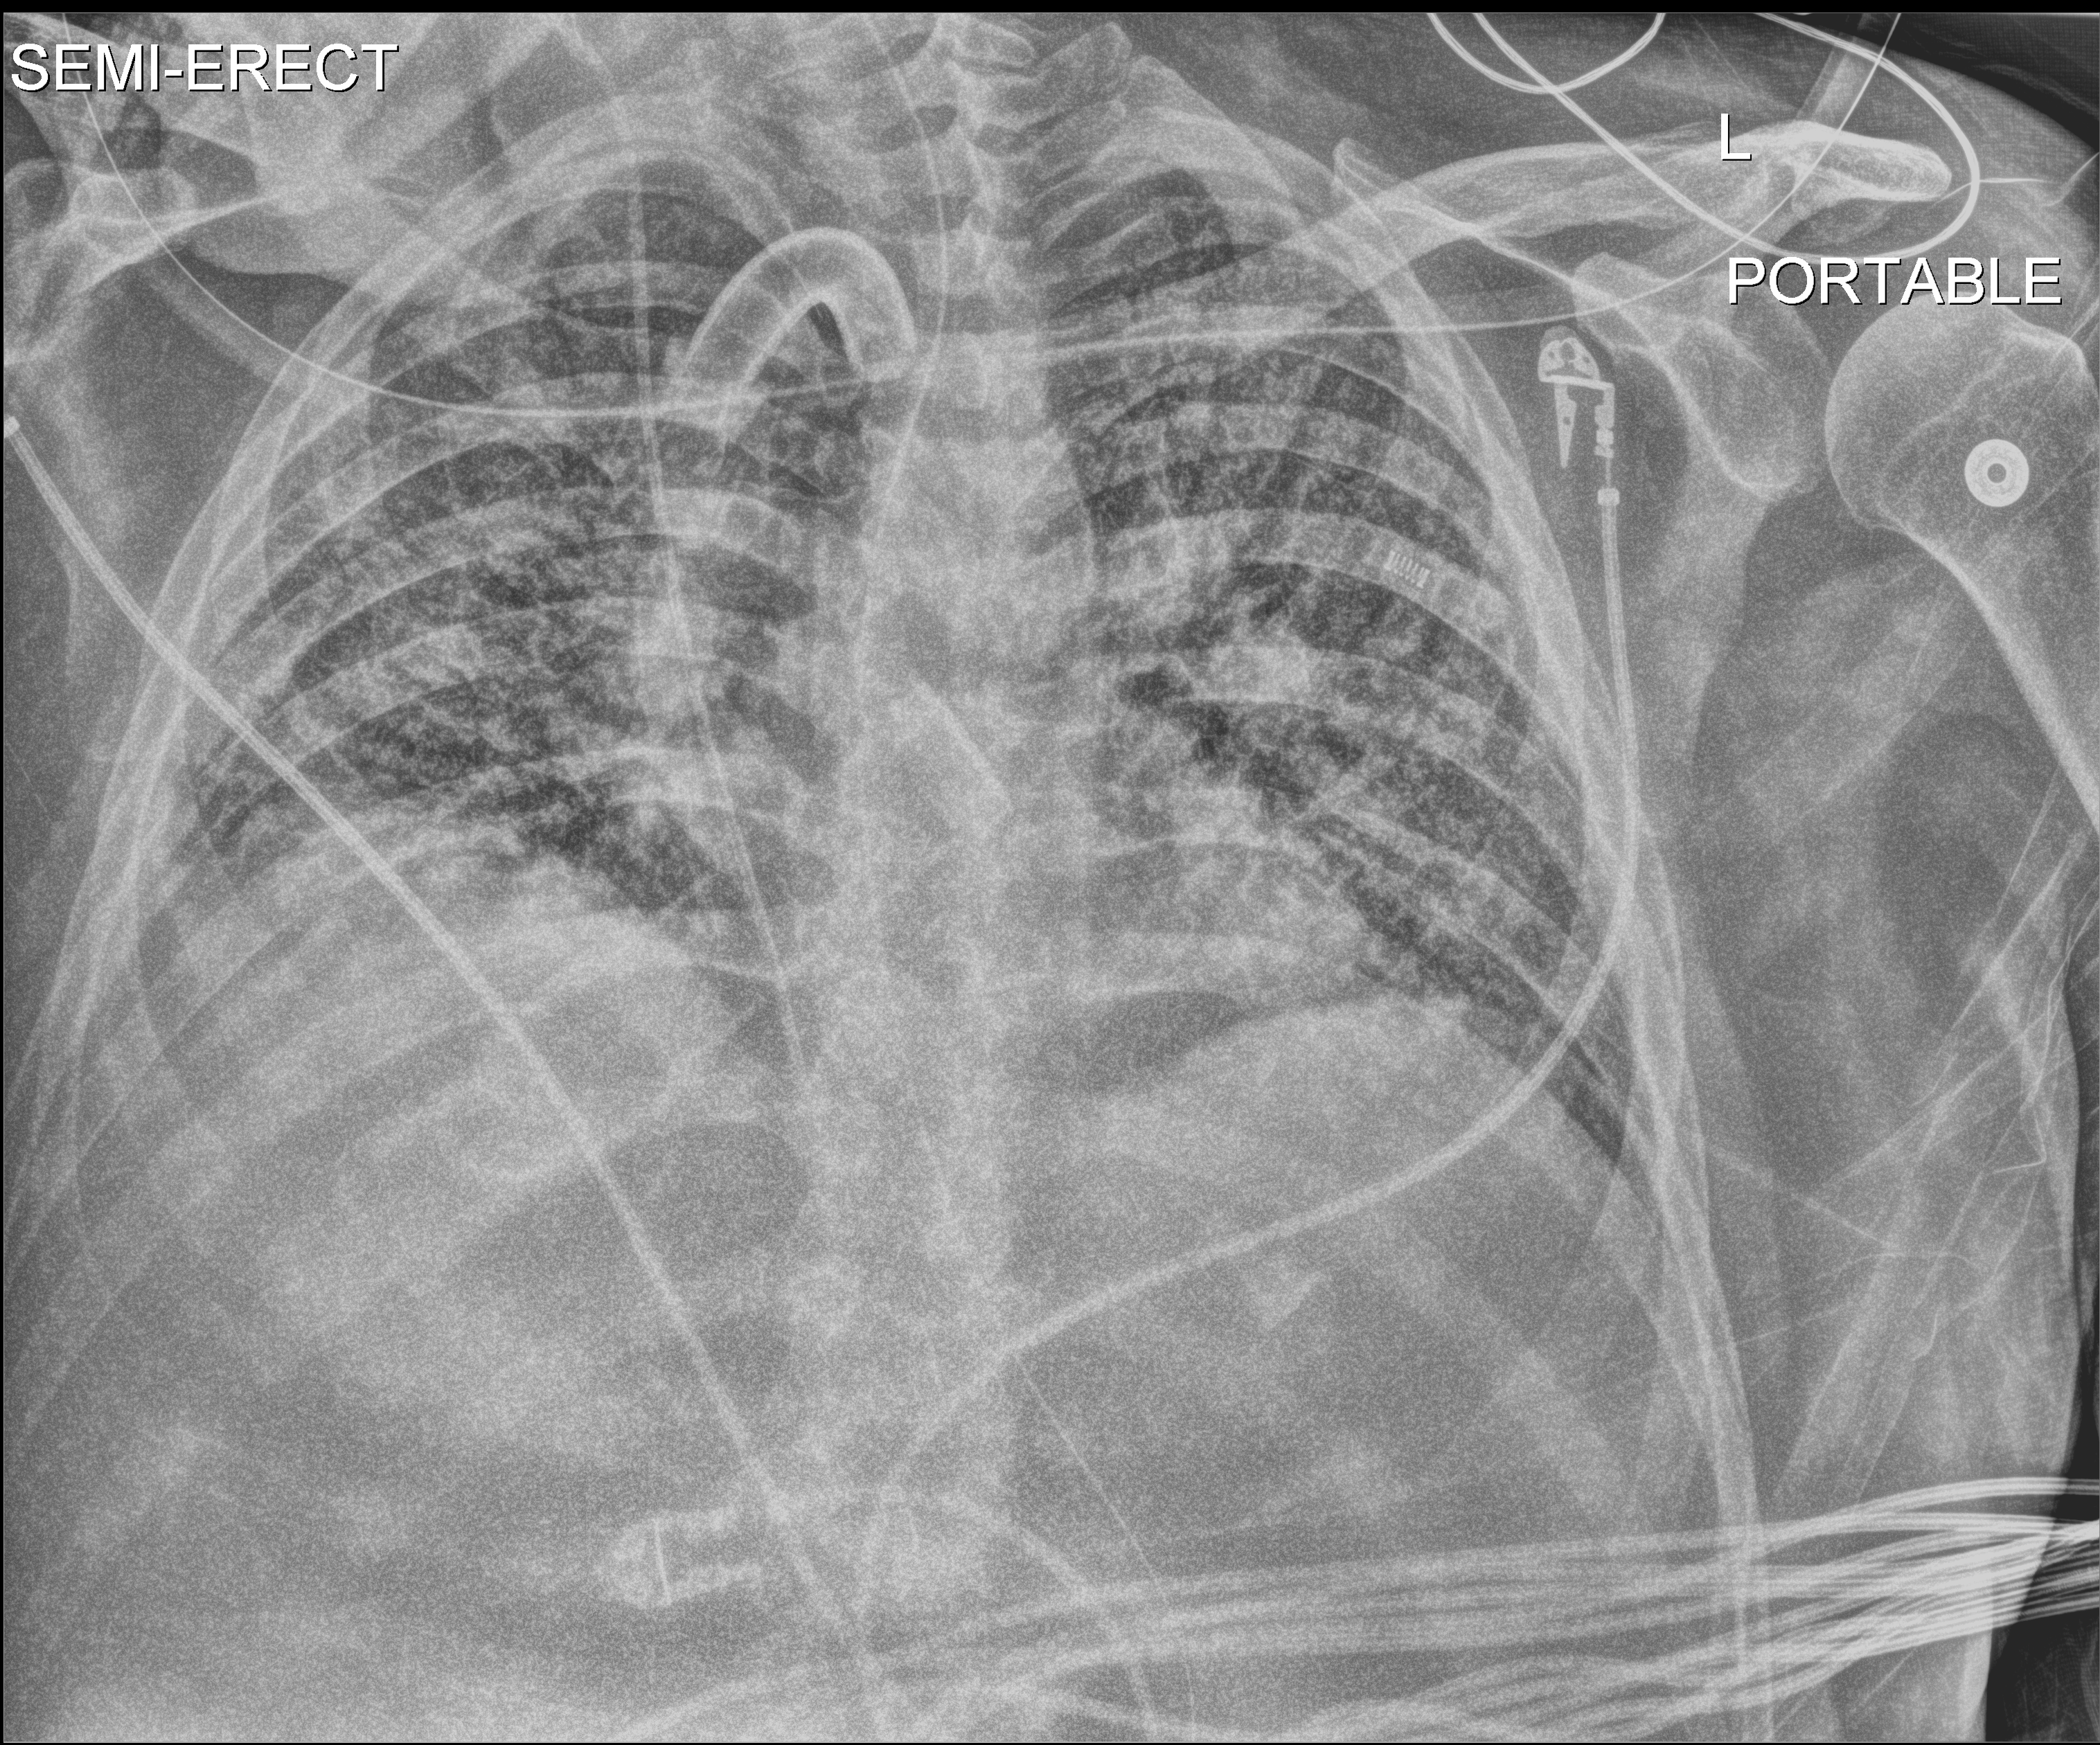
Chest radiograph, anteroposterior (AP) projection. Male patient hospitalised with COVID-19, age 18–59 years.
Hospital-stay facts (about this admission, not read from this image; timing relative to this image not recorded):
- length of hospital stay: 80 days
- admitted to intensive care during this hospital stay: yes
- hypertension (admission record): yes